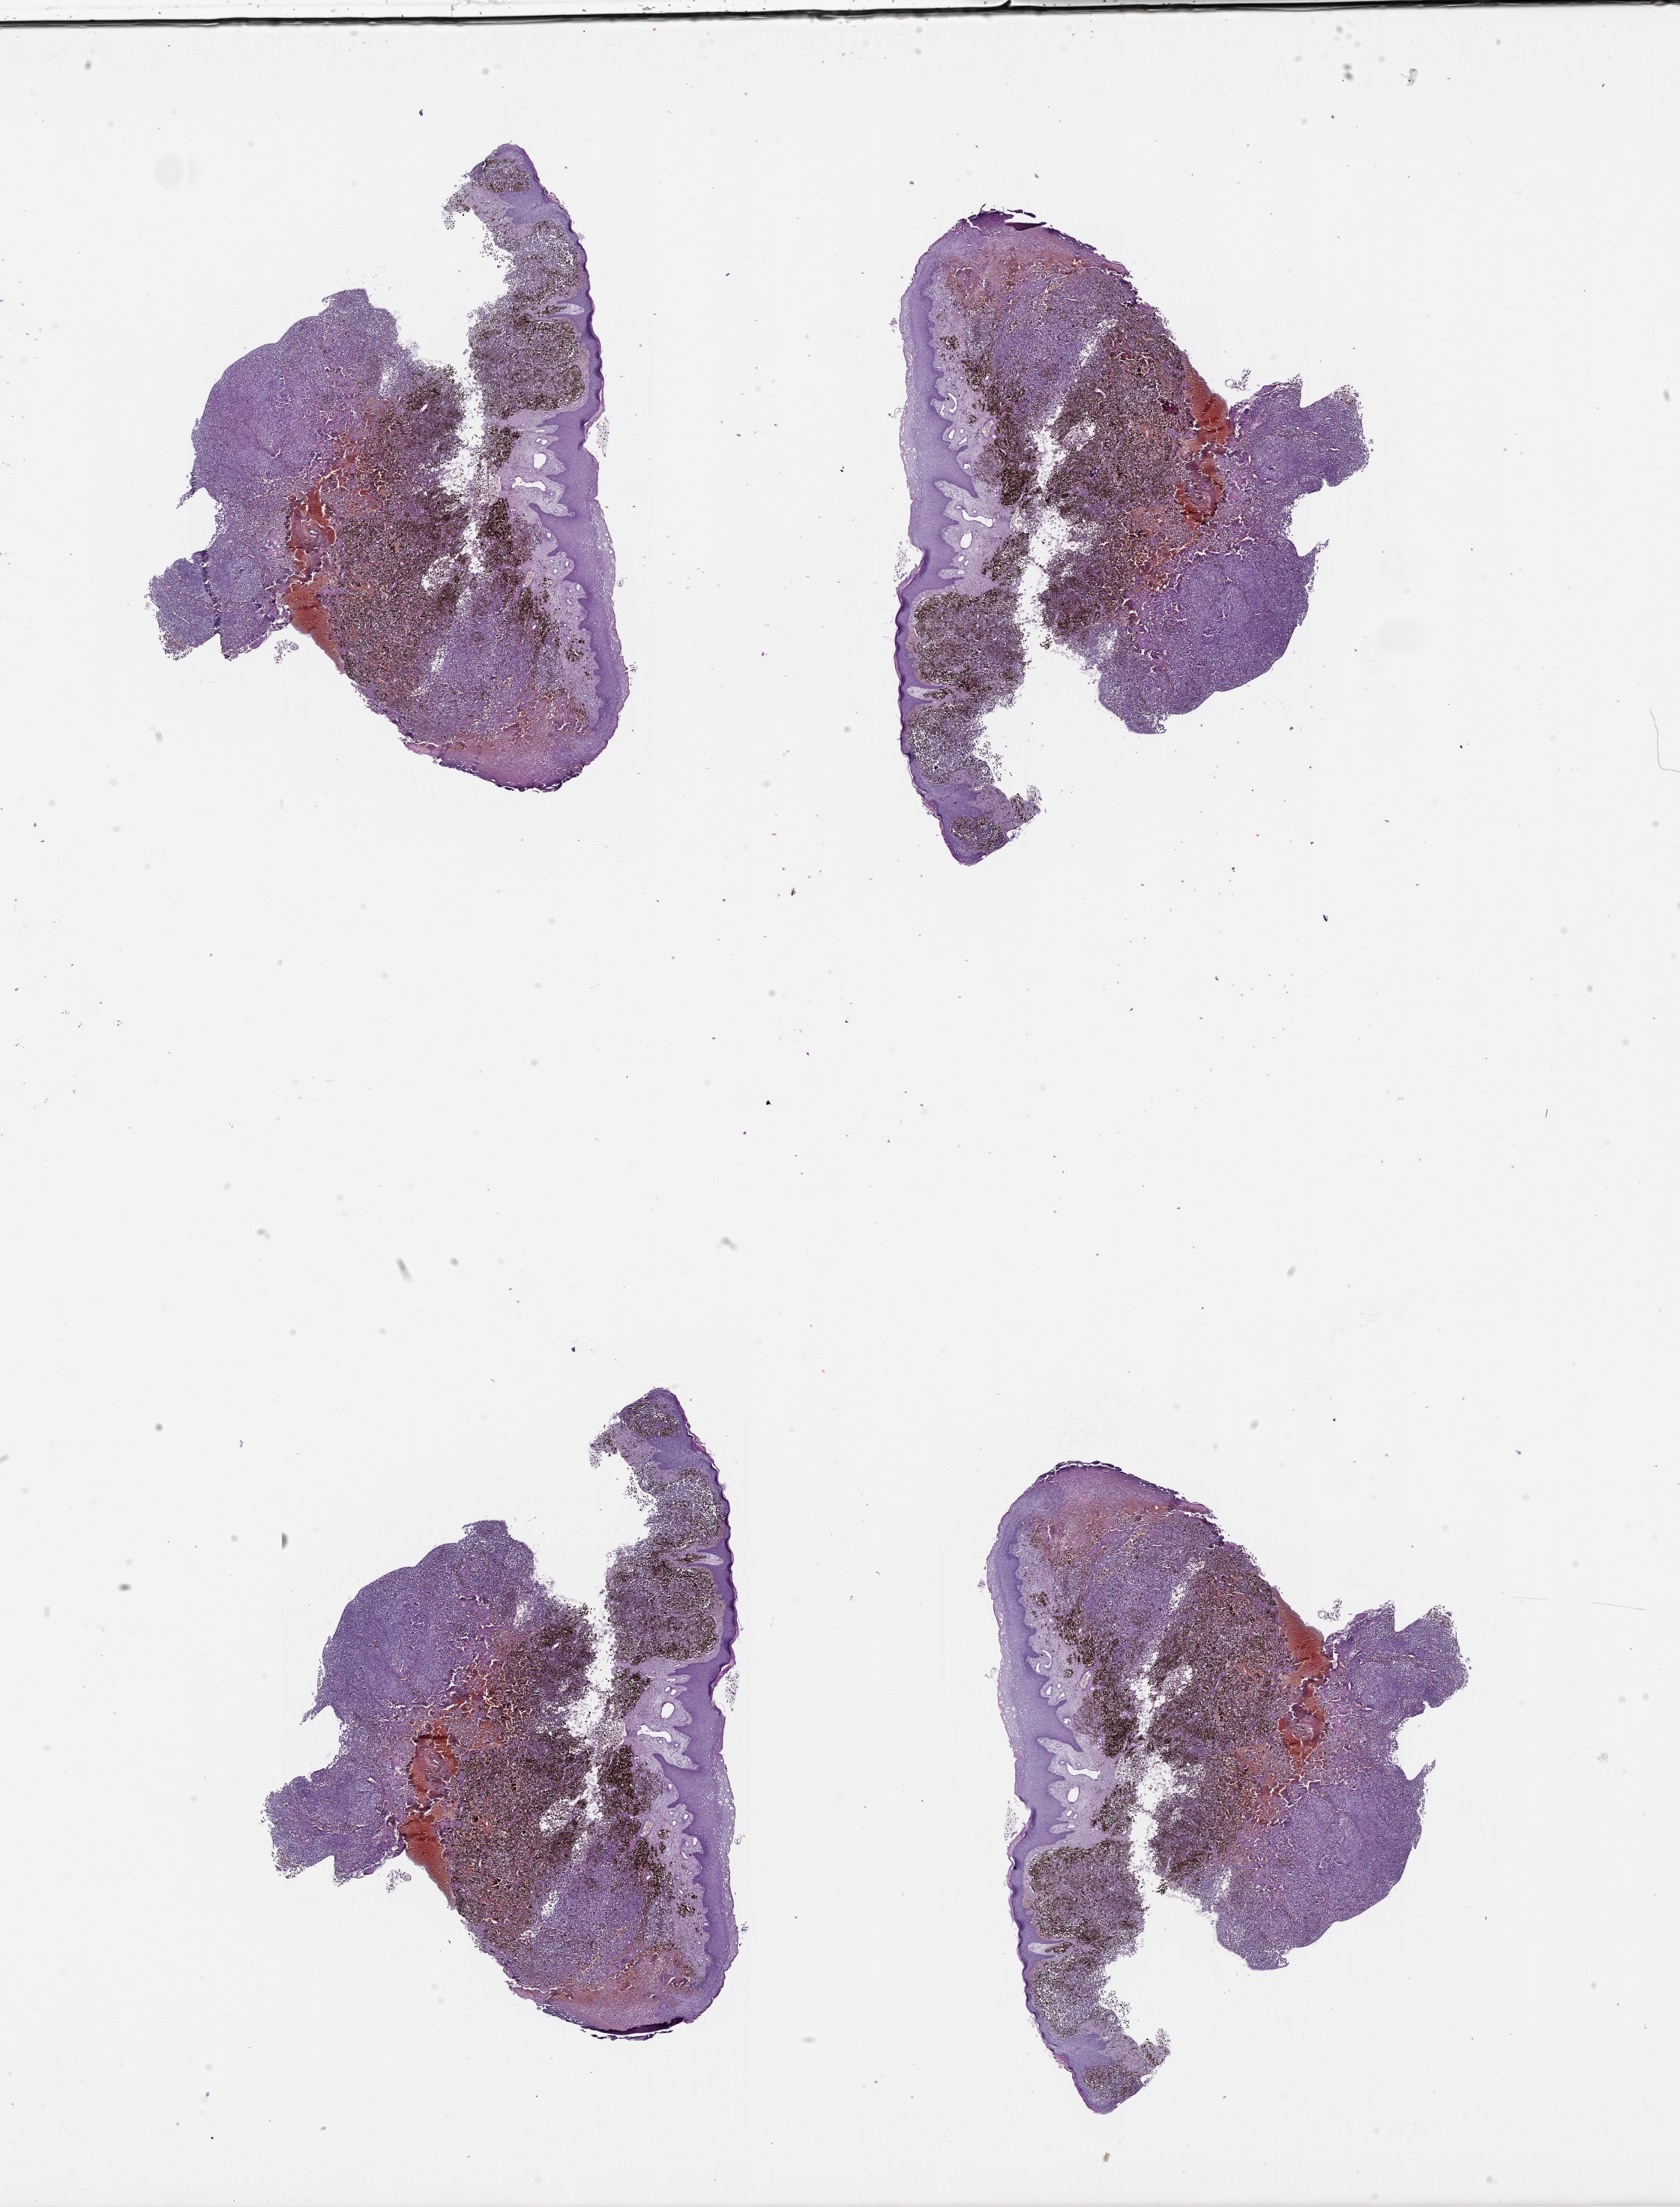
Hematoxylin and eosin (H&E) stained whole-slide image — shown as a low-resolution overview of the whole scanned area (about 18.0 x 23.7 mm); melanoma tumour tissue; sampled site not recorded. Patient: female, age 81 years.
Diagnosis: Malignant melanoma, NOS. AJCC pathologic stage: IIC. Primary tumour site (as recorded): trunk.